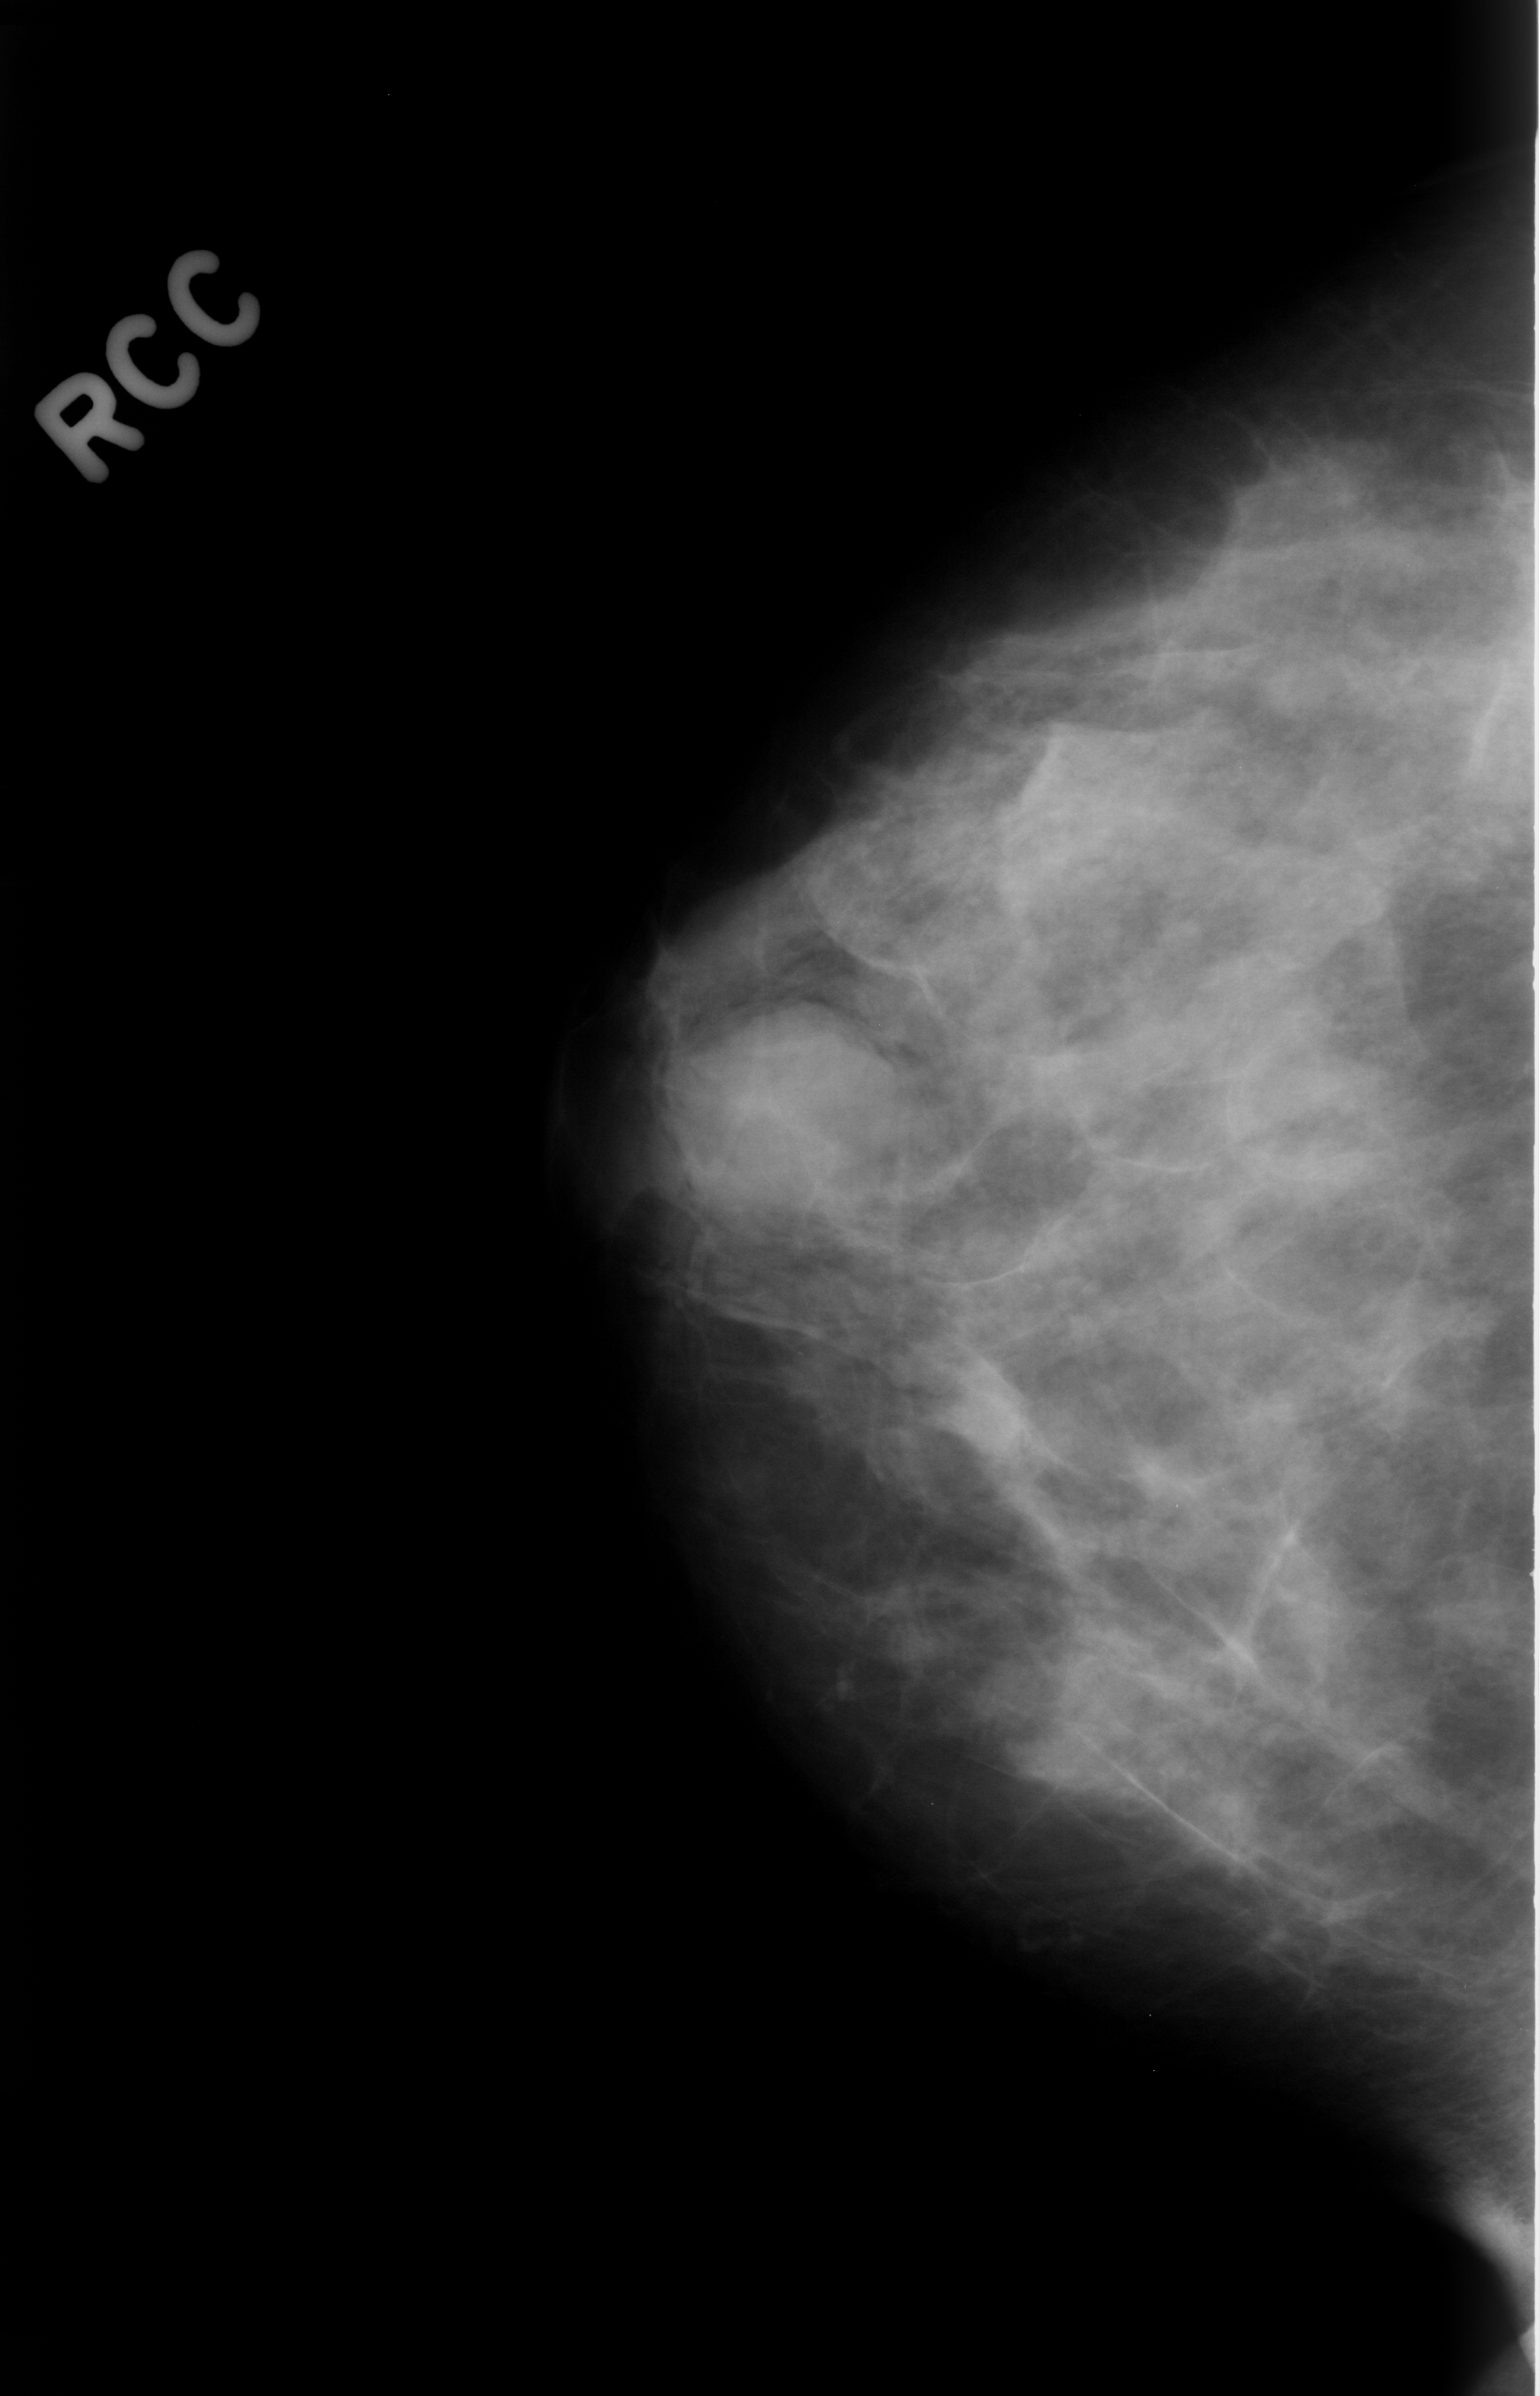
Digitized screen-film mammogram; right breast; craniocaudal (CC) view; breast composition: scattered fibroglandular densities (BI-RADS density category 2 of 4).
Radiologist-marked abnormalities on this image: mass, shape oval, margins circumscribed; BI-RADS assessment category 4; subtlety rating 4 on a 1 (subtle) to 5 (obvious) scale; pathology result (as recorded, not read from the image): benign.